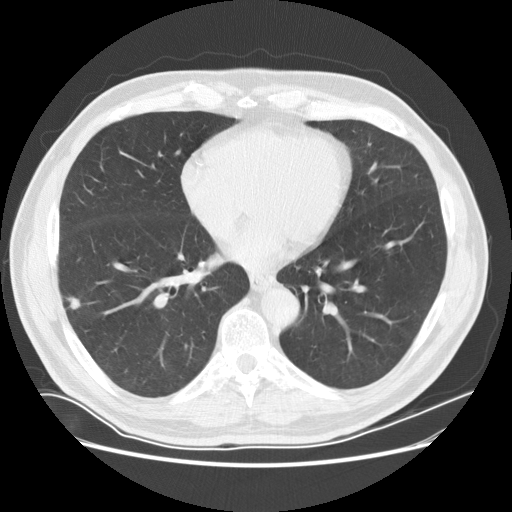
Low-dose screening chest CT, one axial slice; 120 kVp; lung window (W 1500 / L -600 HU); 512 × 512 image matrix.
Outlined on this slice (outlined manually by an expert reader):
- lesion 1 (tumor, lower lobe of right lung): bounding box [x1, y1, x2, y2] px = [66, 297, 81, 310]